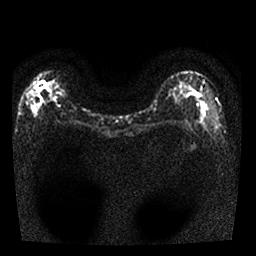
Breast MRI, one axial slice; slice 13 of 25 in the series (ordered by position); diffusion-weighted series; image 2 of 4 stored at this slice position (different b-values; order by instance number); 1.5 T; 4 mm slice thickness; 256 × 256 image matrix, field of view 300 × 300 mm. Female patient.
Annotated regions visible in this slice (expert manual segmentation):
- tumour on diffusion-weighted imaging: bounding box <28,82,46,97> (left, top, right, bottom; pixels)